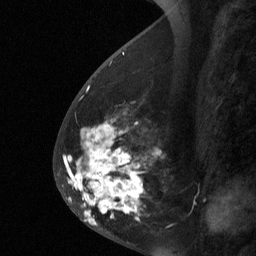
Breast MRI (dynamic contrast-enhanced), one sagittal slice. Position 25 of 64 along the scan axis. Dynamic contrast-enhanced study with each time point stored as its own series, time point 2 of 3 at this slice position (early post-contrast, ordered by acquisition time). 1.5 T. TE 4.8 ms, TR 27 ms. 256 × 256 image matrix, field of view 180 × 180 mm. Female patient, age 56 years. From the clinical record (not read from this slice): setting: breast cancer imaged before/during neoadjuvant chemotherapy; receptor status: HER2-positive.
Annotated regions visible in this slice (semi-automatic segmentation, software-assisted and operator-edited):
- analysis volume of interest (the breast-tissue region the enhancement analysis was run in; not a lesion): bounding box <59,104,161,229> (left, top, right, bottom; pixels)
- tumour enhancement mask (voxels above the 90 % enhancement threshold inside the analysis volume of interest): <68,125,143,226>